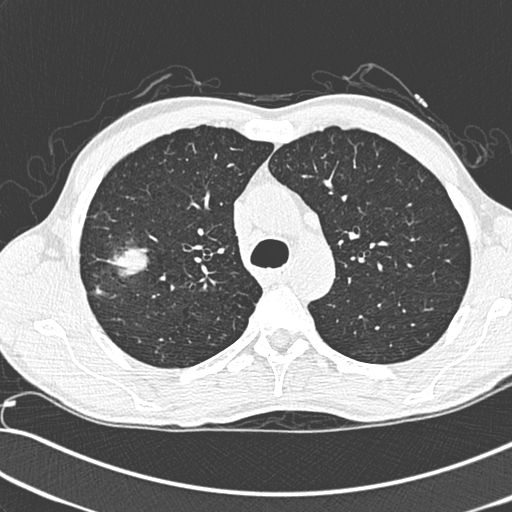
Low-dose screening chest CT, one axial slice. 120 kVp. Lung window (W 1500 / L -600 HU). 1.3 mm slice thickness. 512 × 512 image matrix.
Annotated regions visible in this slice (expert manual segmentation):
- lesion 1 (tumor, upper lobe of right lung): bounding box <106,247,148,277> (left, top, right, bottom; pixels)